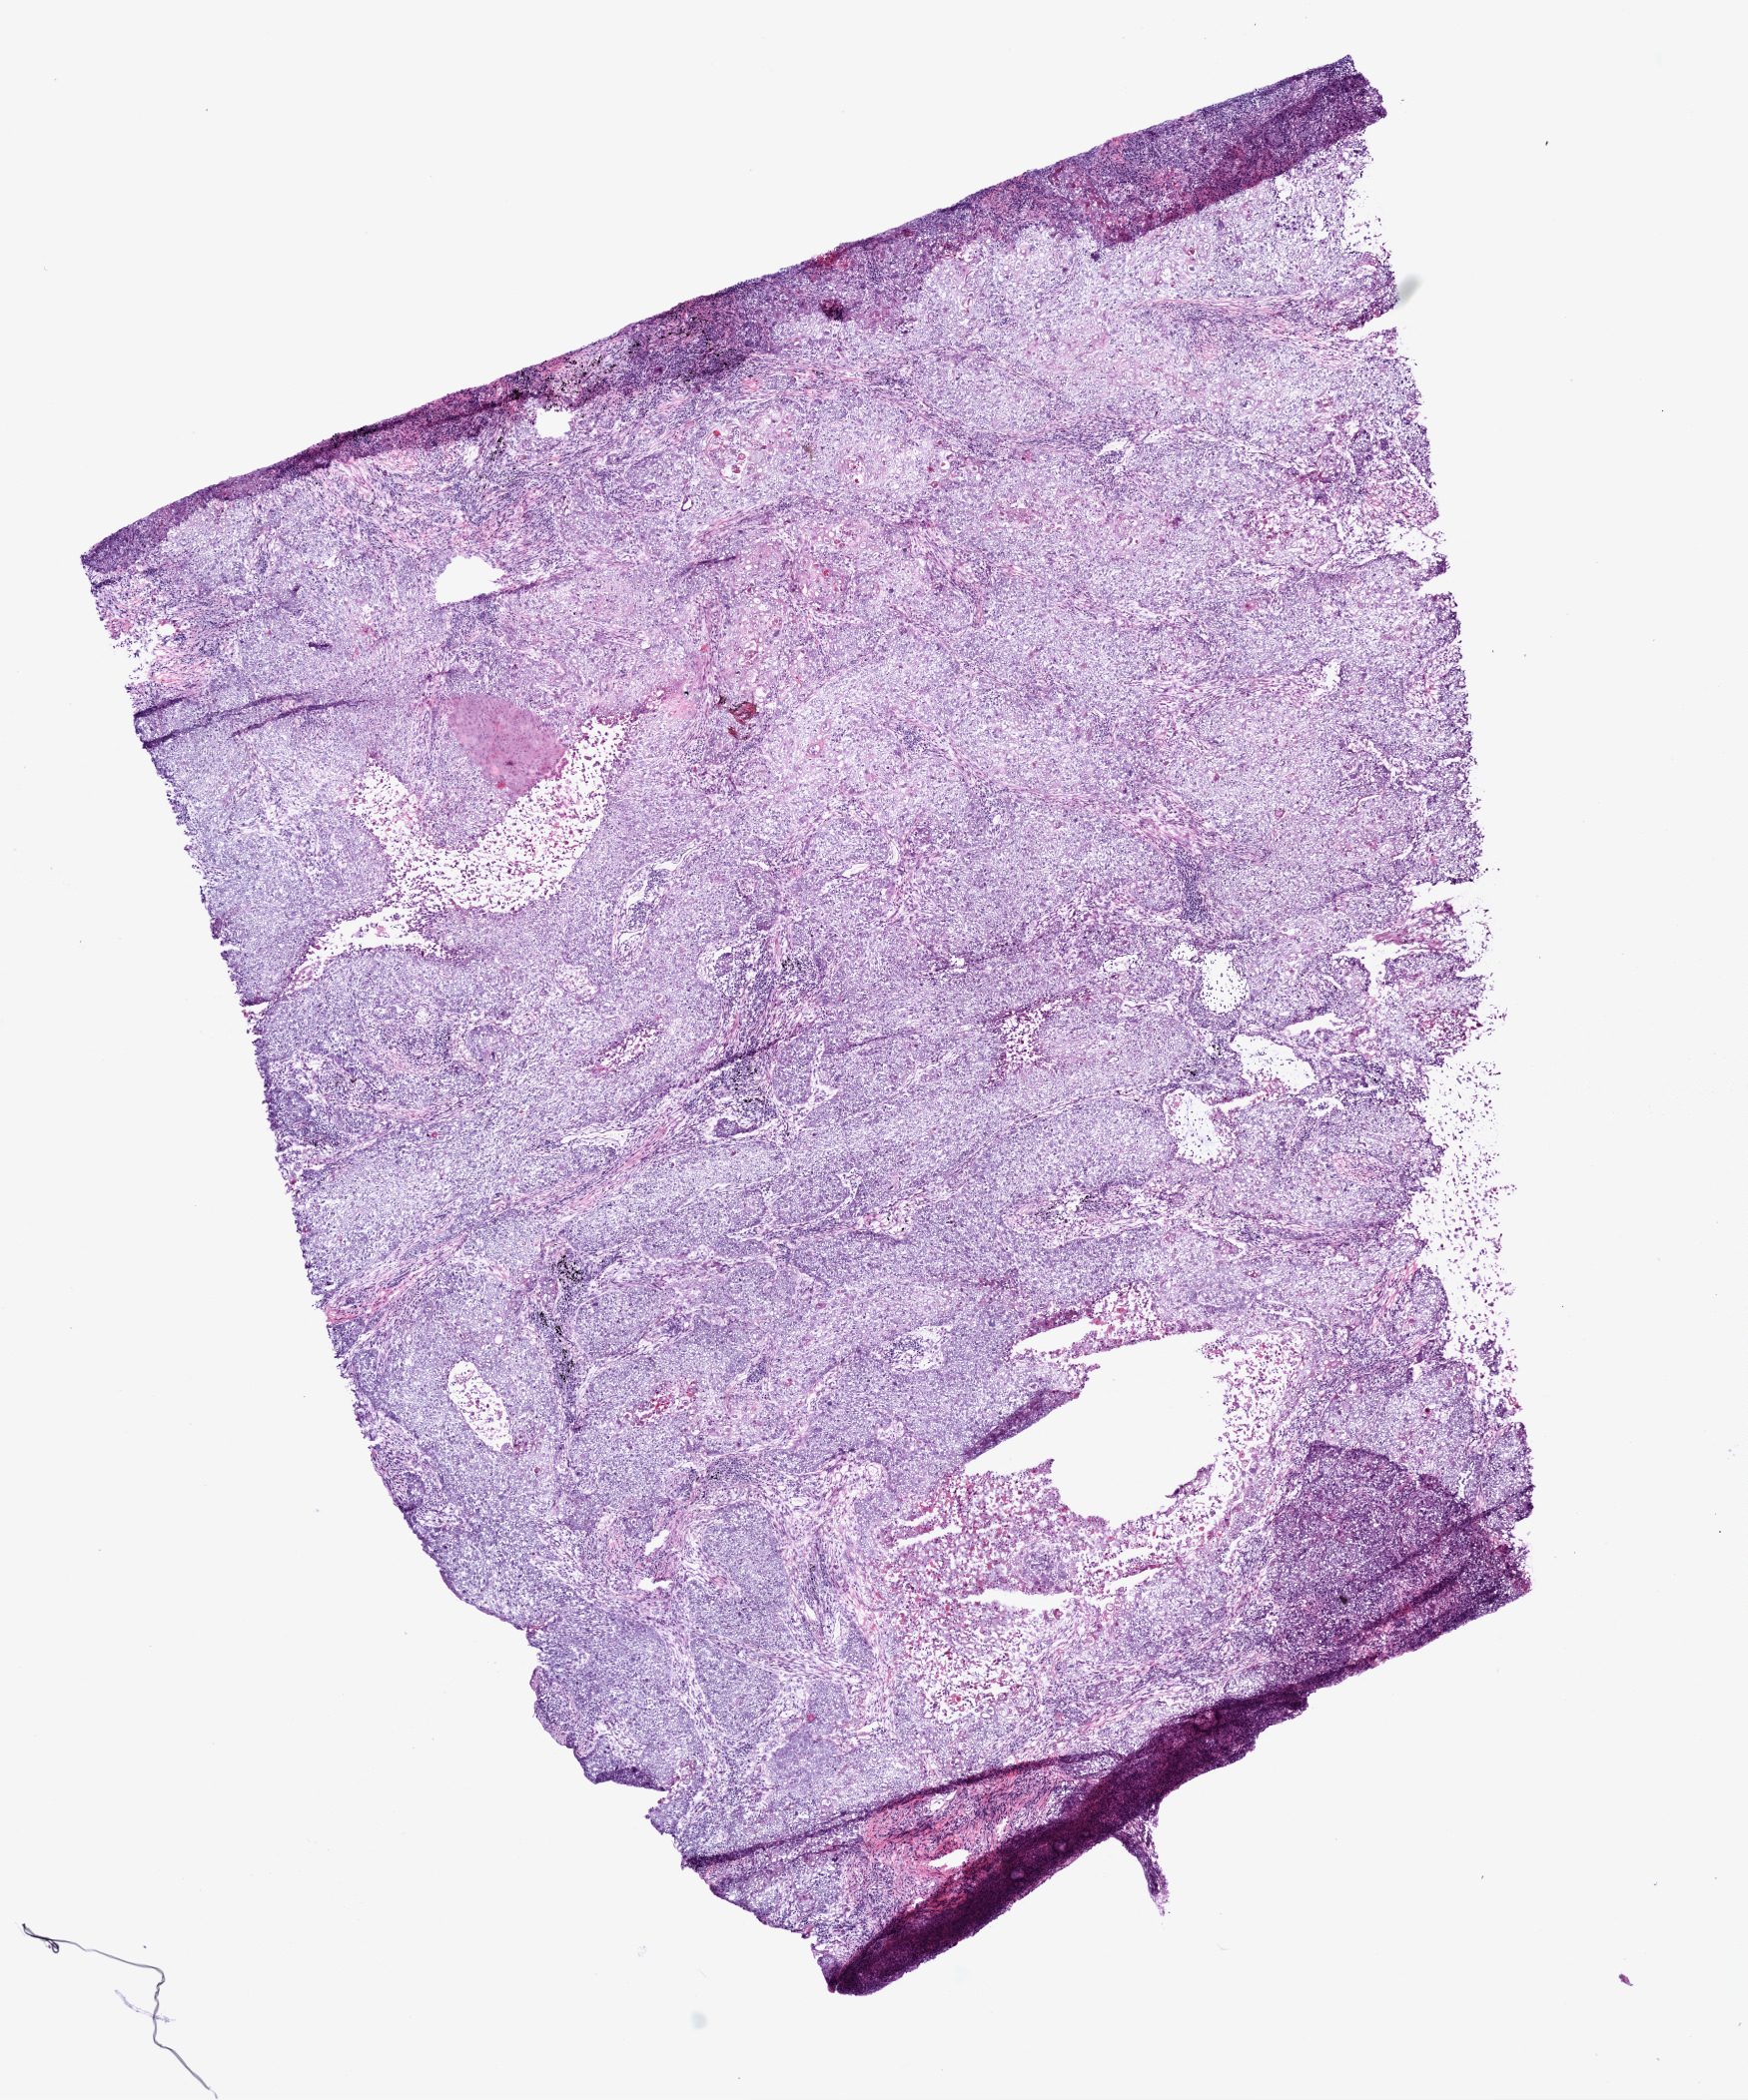
H&E whole-slide image, a low-resolution overview of the entire scanned area, about 7.0 x 8.4 mm. Frozen section. Sample: primary tumour, lung. Male patient; age at initial diagnosis 77 years. Composition of this section per pathologist review: tumour cells 85%, tumour nuclei 90%, normal cells 0%, stromal cells 12%, necrosis 3%. Infiltration values recorded for this section: lymphocyte infiltration 3%.
* pathologic diagnosis: Squamous cell carcinoma, NOS (upper lobe, lung)
* AJCC pathologic stage: IB